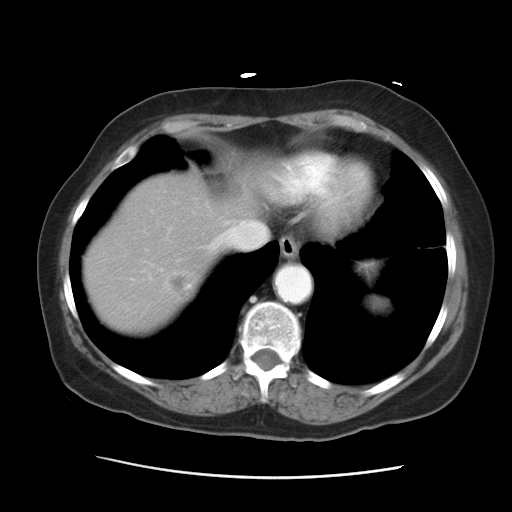
Contrast-enhanced abdominal CT, one axial slice; reconstruction kernel STANDARD; soft-tissue window (W 400 / L 40 HU); 7.5 mm slice thickness; 512 × 512 image matrix, field of view 354 × 354 mm. Female patient, age 64 years. From the clinical record (not read from this slice): diagnosis: colorectal cancer liver metastases, imaged before liver resection; multiple liver metastases: no; largest metastasis: 2.5 cm.
Outlined on this slice (outlined manually by an expert reader):
- hepatic veins: bounding box (x1, y1, x2, y2) in pixels: (210, 220, 266, 249)
- liver: (83, 173, 254, 332)
- planned liver remnant (the part of the liver to remain after resection): (86, 174, 254, 269)
- liver metastasis: (171, 274, 187, 294)